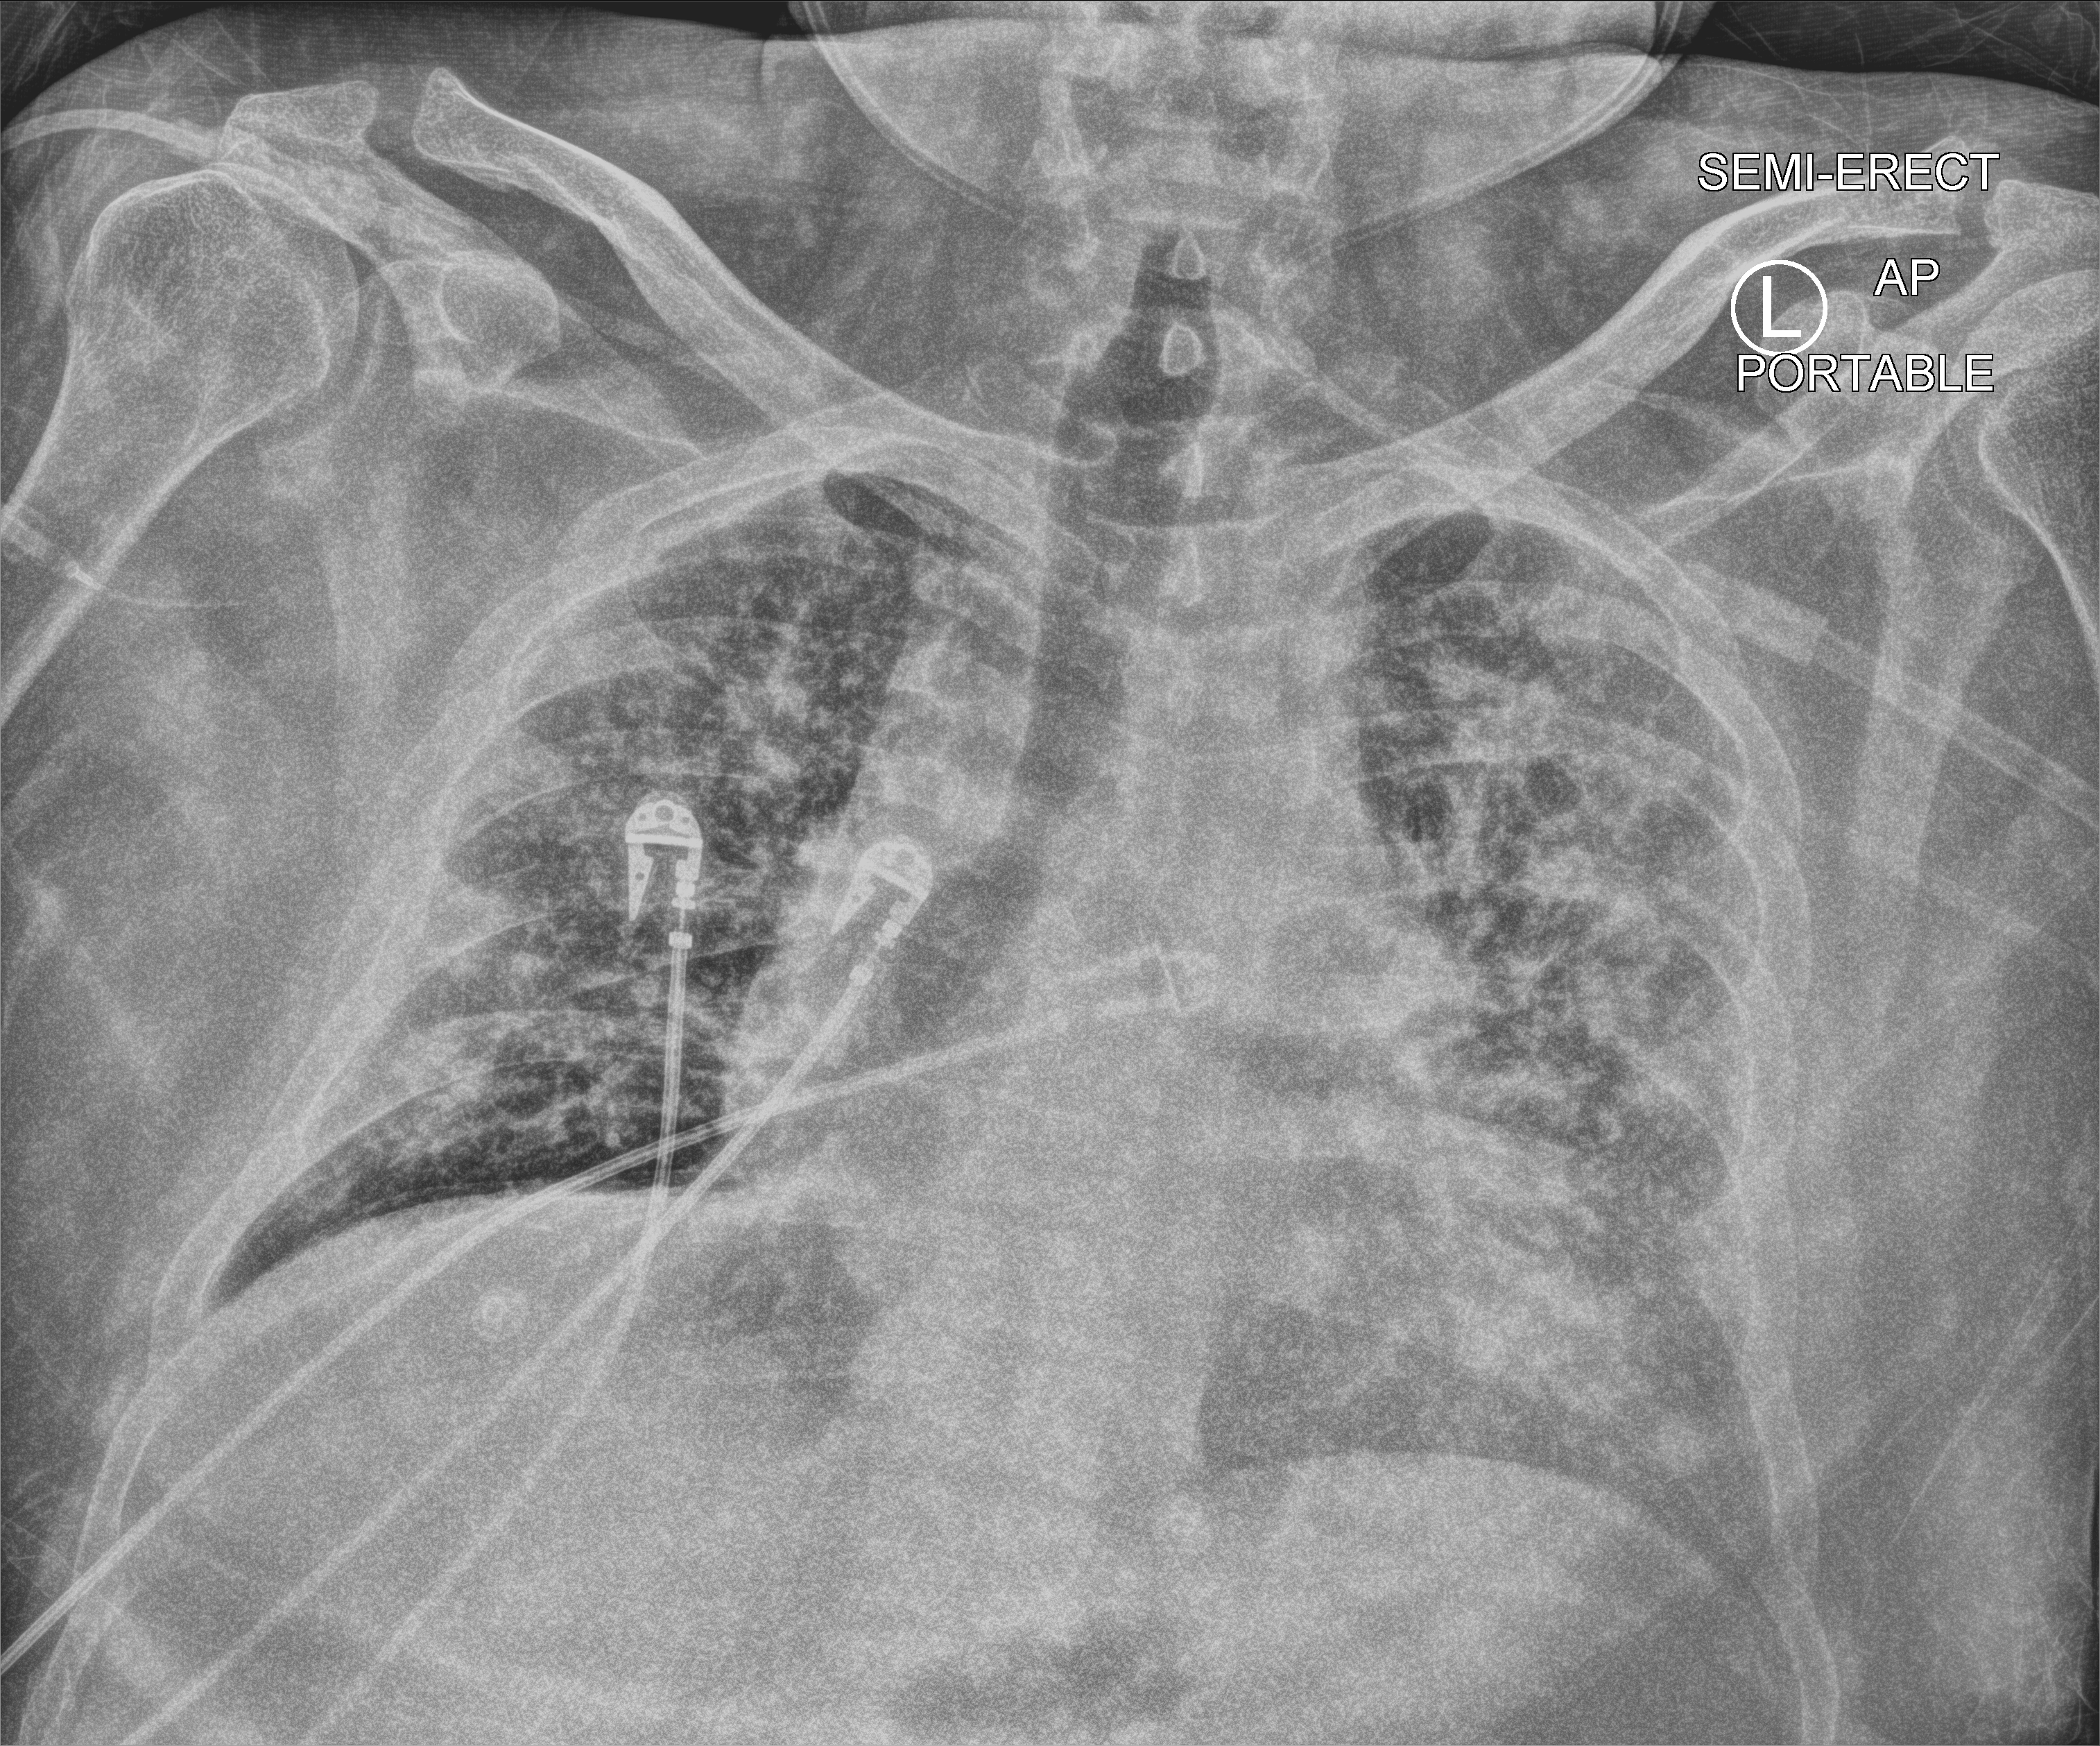
Portable chest radiograph. Patient hospitalised with COVID-19; male, aged 18–59 years.
Hospital-stay facts (about this admission, not read from this image; timing relative to this image not recorded): smoking status (admission record): former.